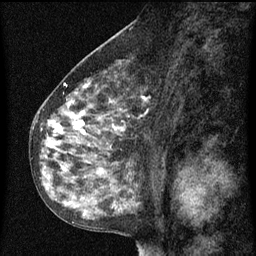
Breast MRI (dynamic contrast-enhanced), one sagittal slice. Position 39 of 60 along the scan axis. Dynamic contrast-enhanced series, image 2 of 3 at this slice position (ordered by acquisition). 1.5 T. TE 4.2 ms, TR 8 ms. 2 mm slice thickness. 256 × 256 image matrix. Patient: female, 55 years.
Annotated regions visible in this slice (semi-automatic segmentation, software-assisted and operator-edited):
- analysis volume of interest (the breast-tissue region the enhancement analysis was run in; not a lesion): bounding box [x1, y1, x2, y2] px = [34, 68, 155, 151]
- tumour enhancement mask (voxels above the 70 % enhancement threshold inside the analysis volume of interest): [48, 82, 151, 149]